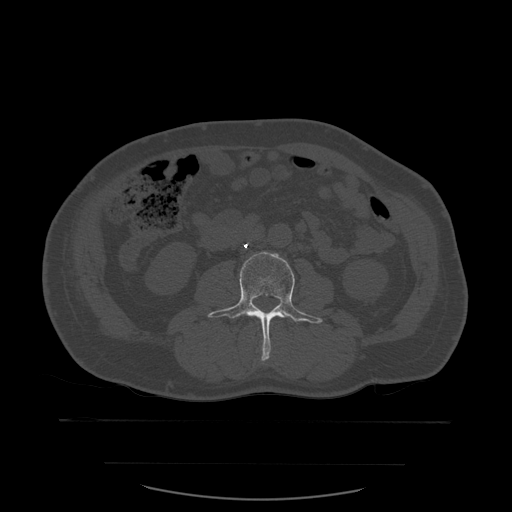
CT including the spine, one axial slice; position 194 of 590 along the scan axis; bone window (W 1800 / L 400 HU); 1.25 mm slice thickness; 512 × 512 image matrix, field of view 479 × 479 mm. Patient age 71 years. From the clinical record (not read from this slice): primary cancer: lung.
Structures marked on this image (semi-automatically segmented with operator editing):
- L3 vertebra: bounding box <208,252,323,361> (left, top, right, bottom; pixels)